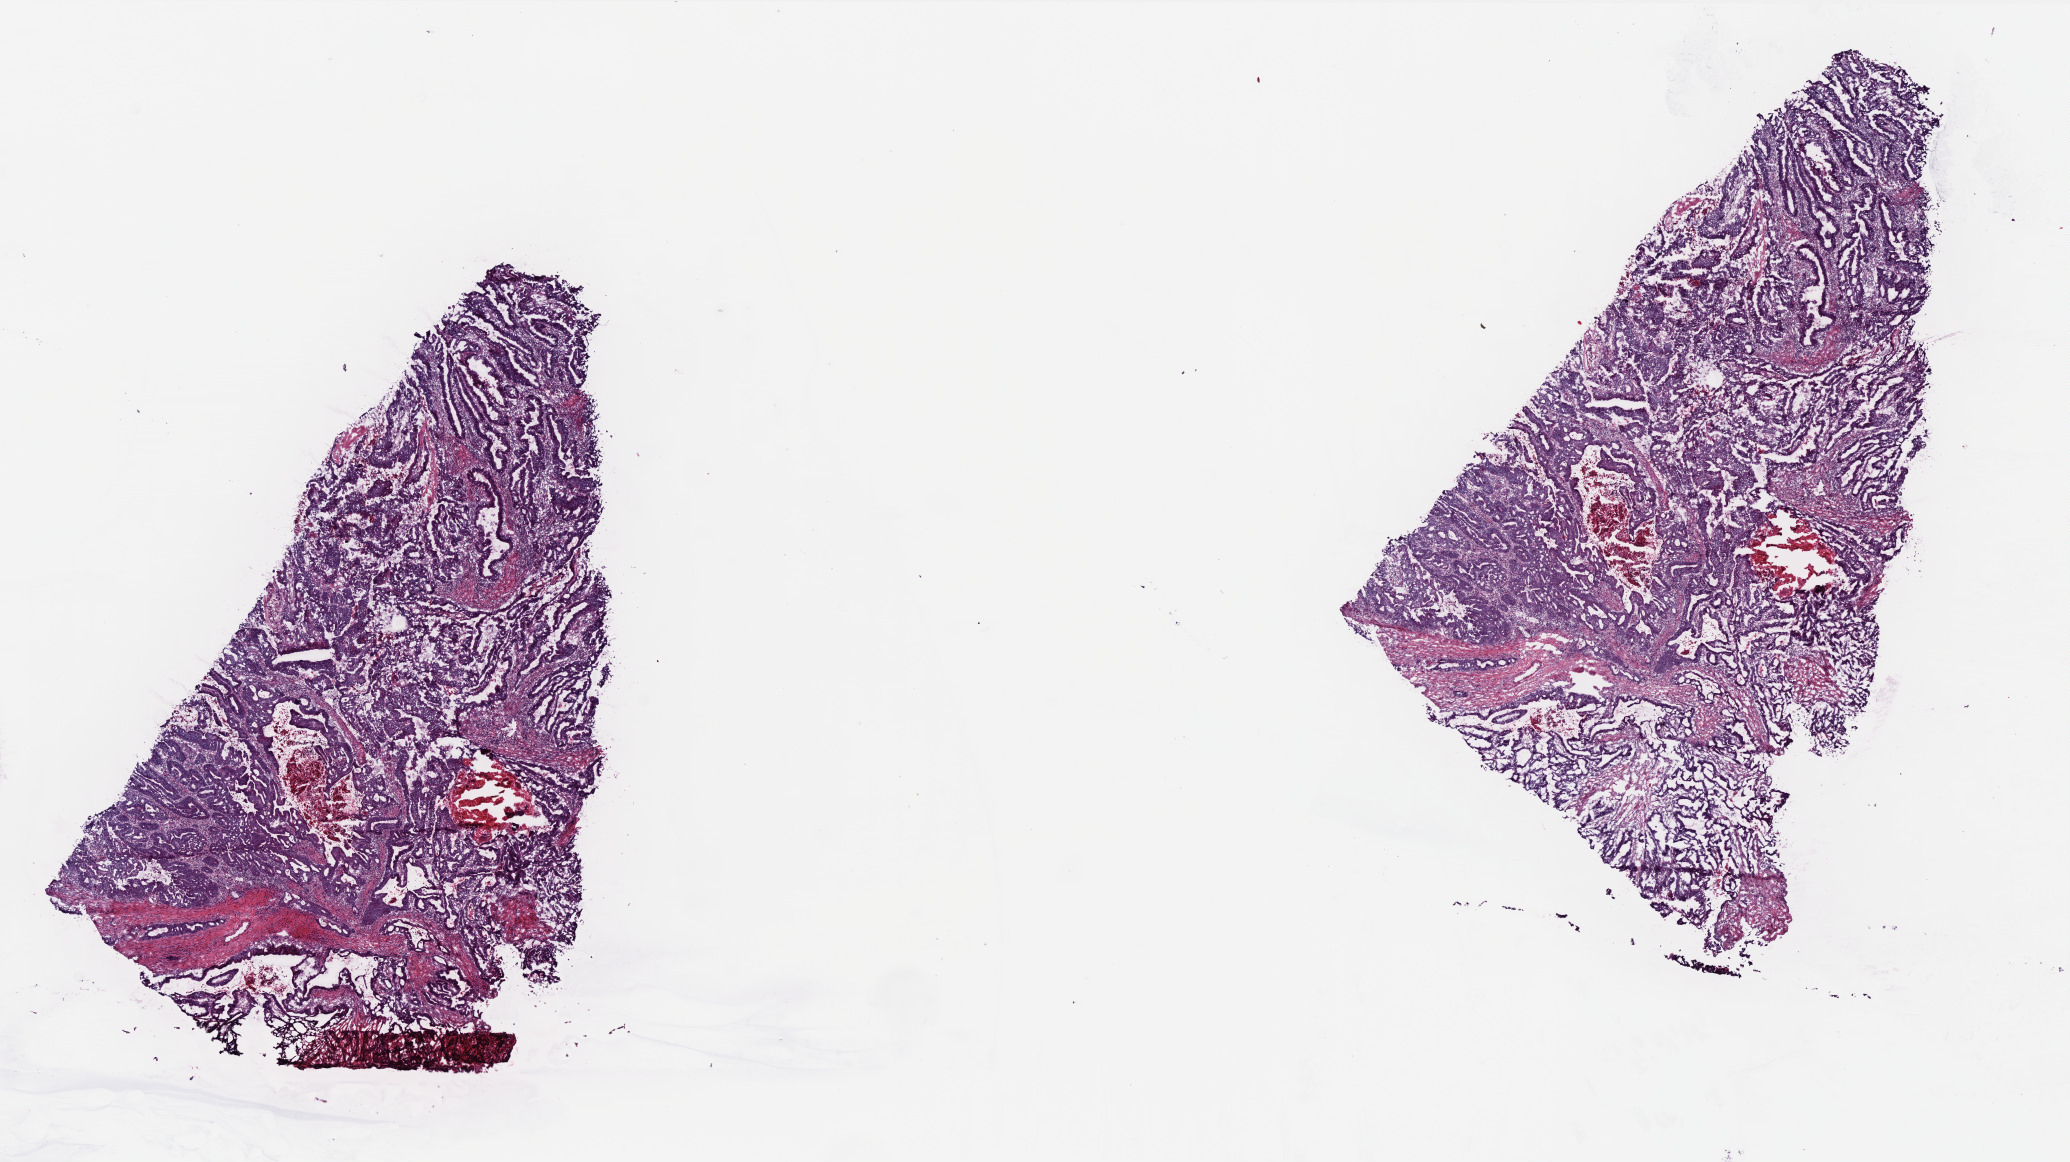
Digitized Hematoxylin and eosin (H&E) stained tissue section (whole slide), whole scanned area (about 16.6 x 9.3 mm, from a 40x scan) shown as a low-resolution overview; frozen section; rectum, primary tumour sample. Female patient; age at initial diagnosis 49 years. Composition of this section per pathologist review: tumour cells 95%, tumour nuclei 80%, normal cells 0%, stromal cells 4%, necrosis 1%. Inflammatory infiltration, as recorded: lymphocyte infiltration 3%, monocyte infiltration 1%, neutrophil infiltration 1%.
AJCC pathologic stage: IIIB (6th edition). Diagnosis: Adenocarcinoma, NOS. Lymph nodes positive (case pathology): 1 of 24 examined.